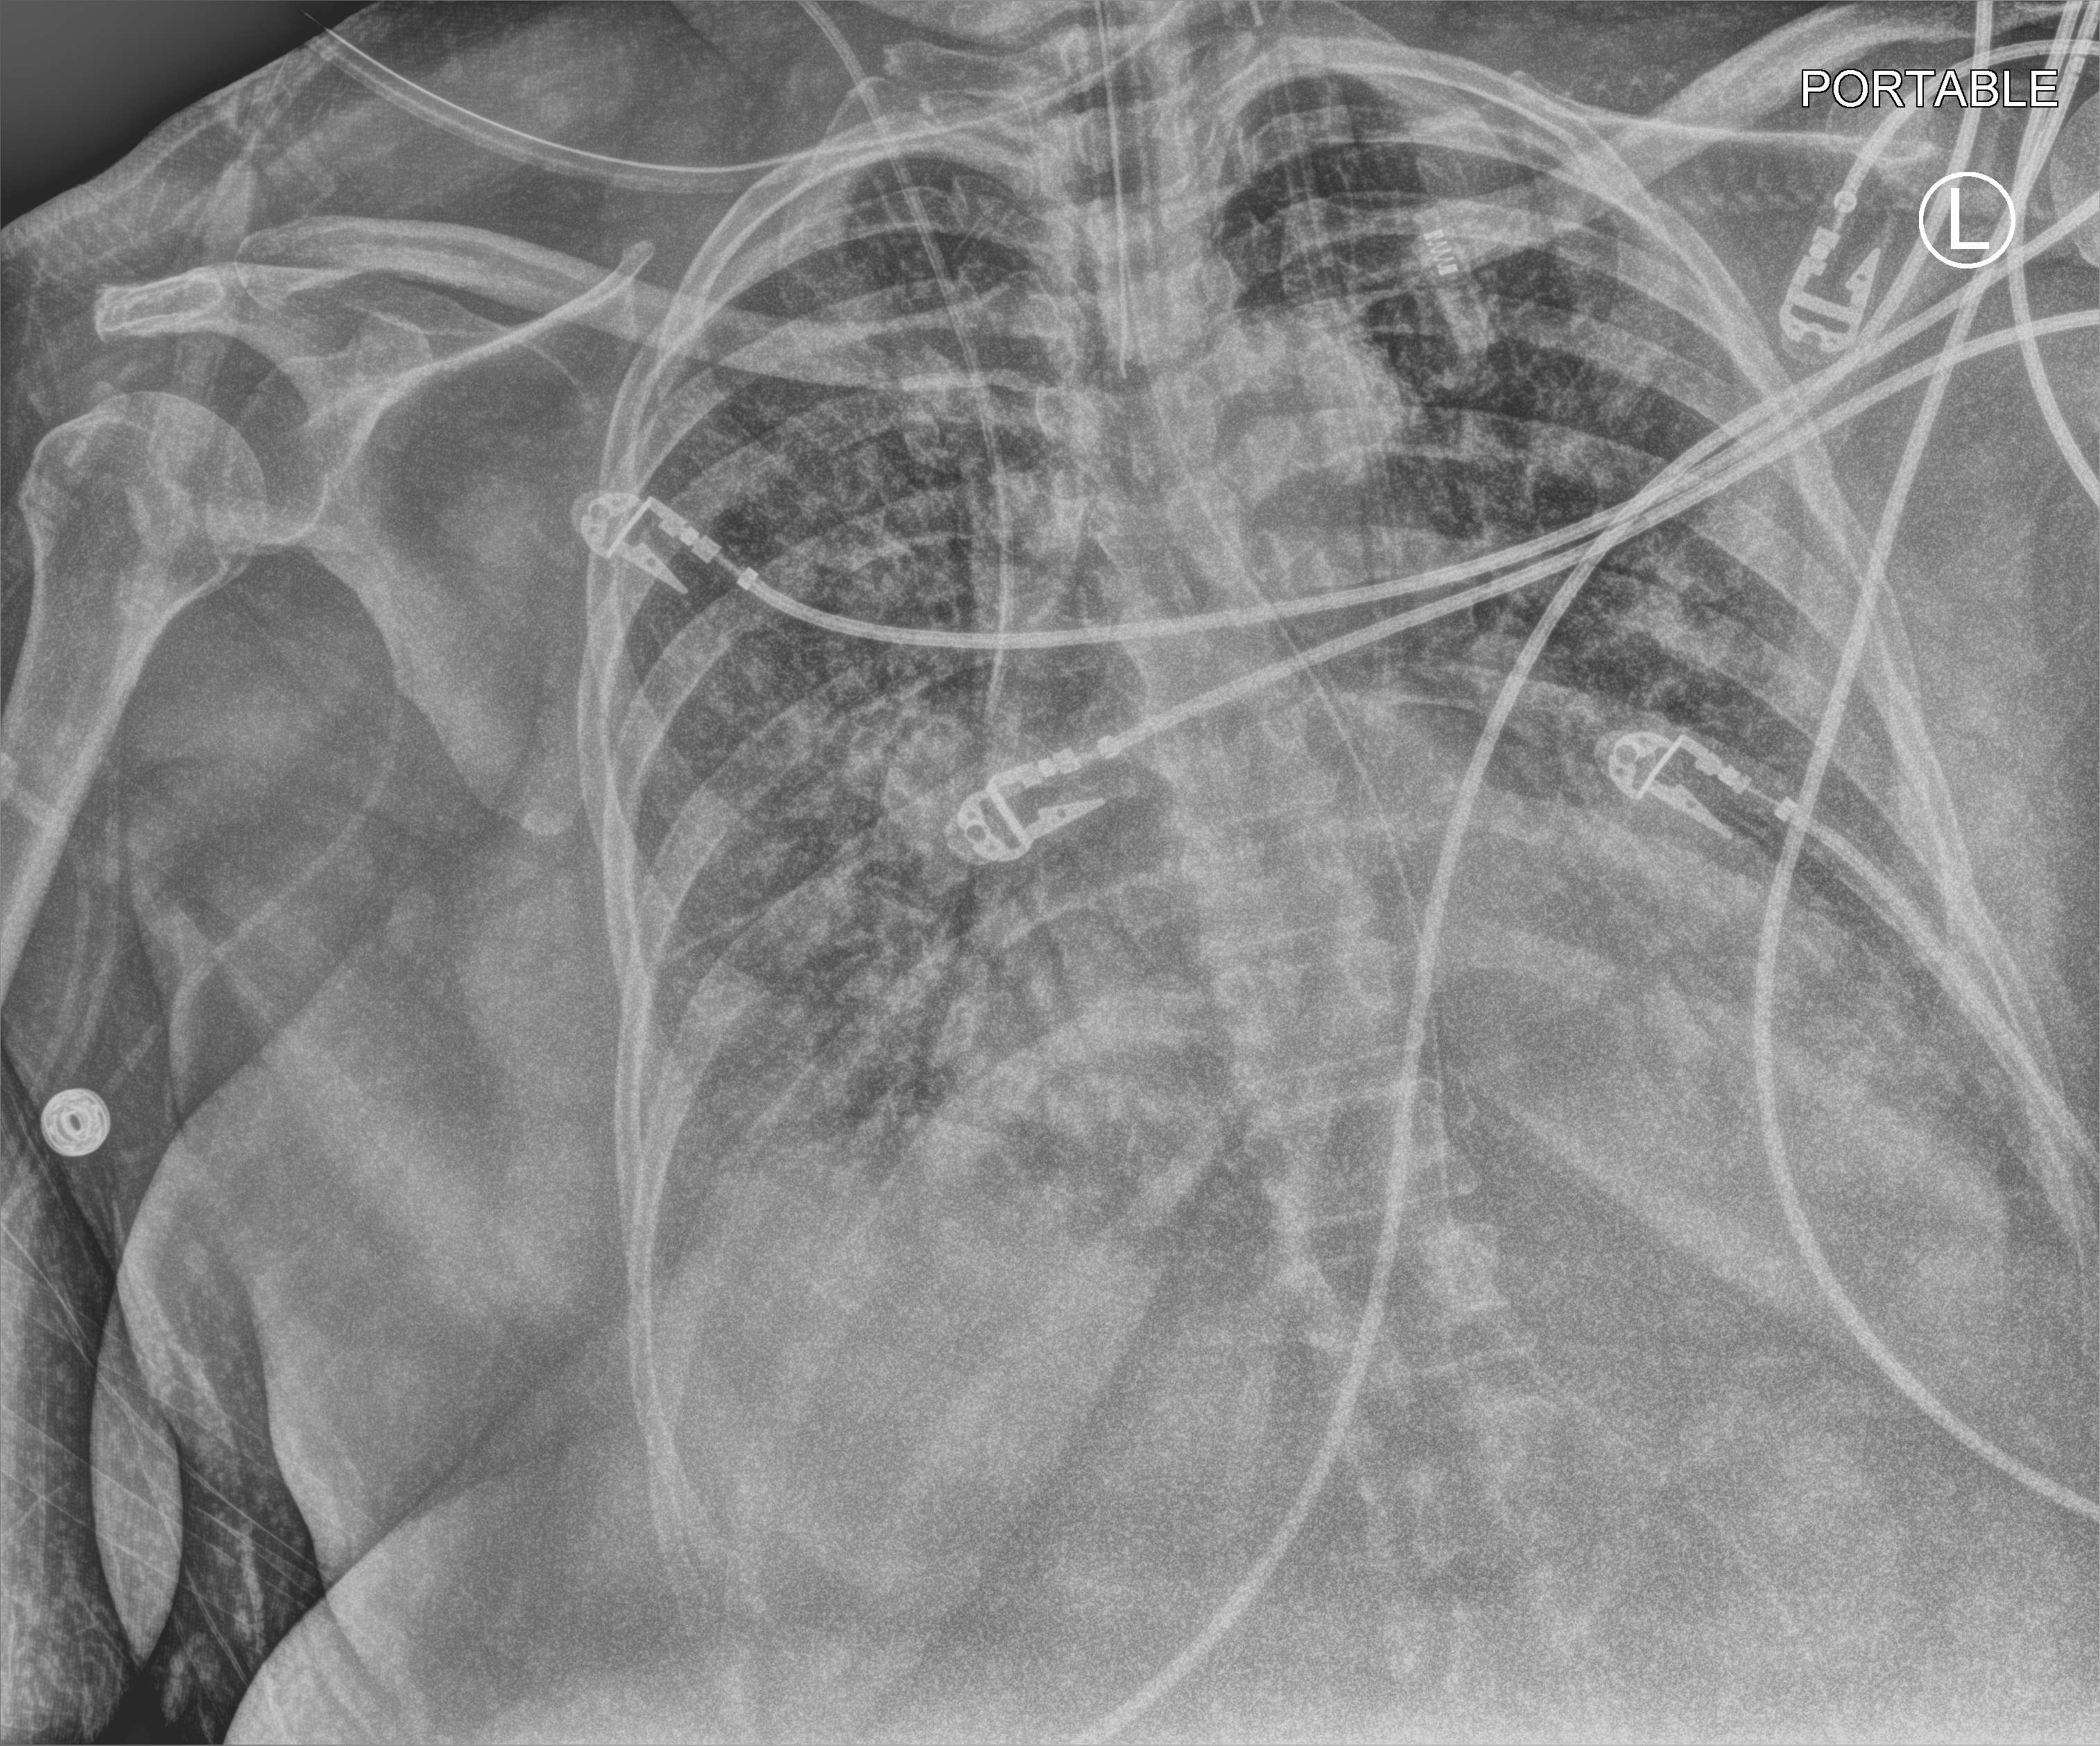
Chest X-ray (portable), anteroposterior (AP) projection. Female patient hospitalised with COVID-19, age 60–74 years.
From the hospital-stay record, not from the radiograph (when in the stay this image was taken is not recorded):
- mechanically ventilated during this hospital stay: yes
- admitted to intensive care during this hospital stay: yes
- chronic kidney disease (admission record): no